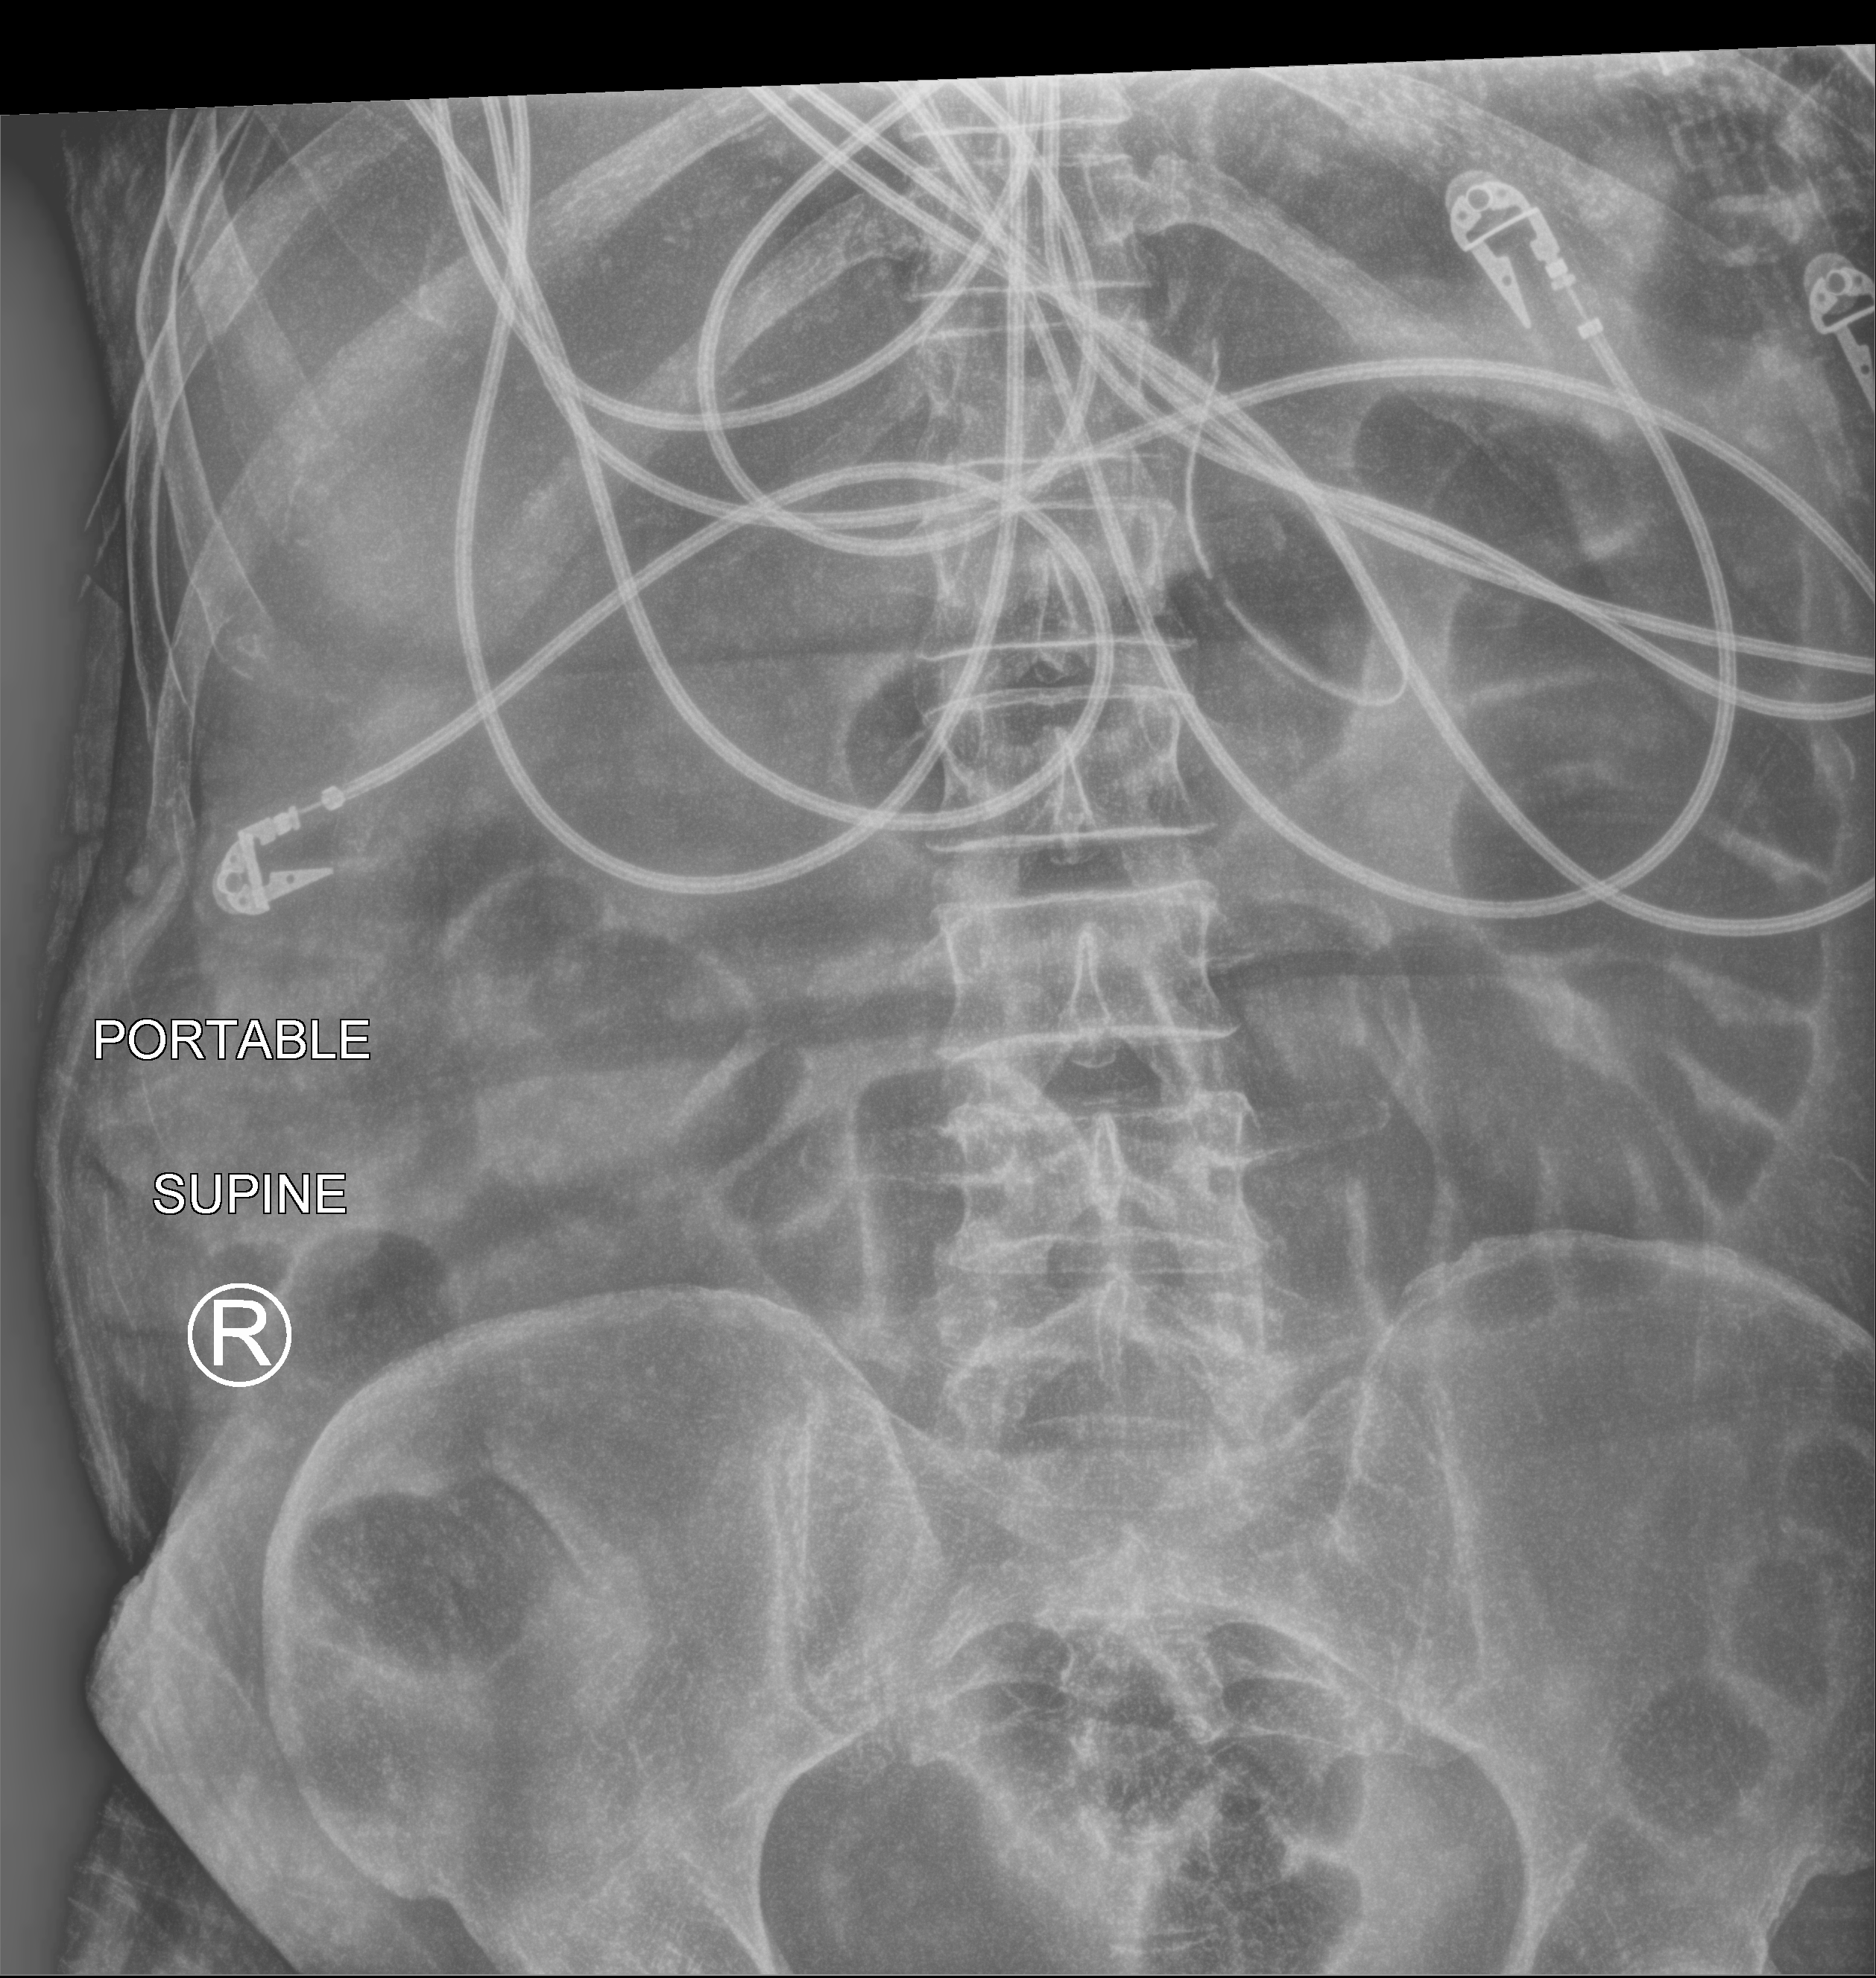
Portable abdomen radiograph, anteroposterior (AP) projection. Patient hospitalised with COVID-19; male, aged 60–74 years.
From the hospital-stay record, not from the radiograph (when in the stay this image was taken is not recorded): admitted to intensive care during this hospital stay: yes; length of hospital stay: 54 days.